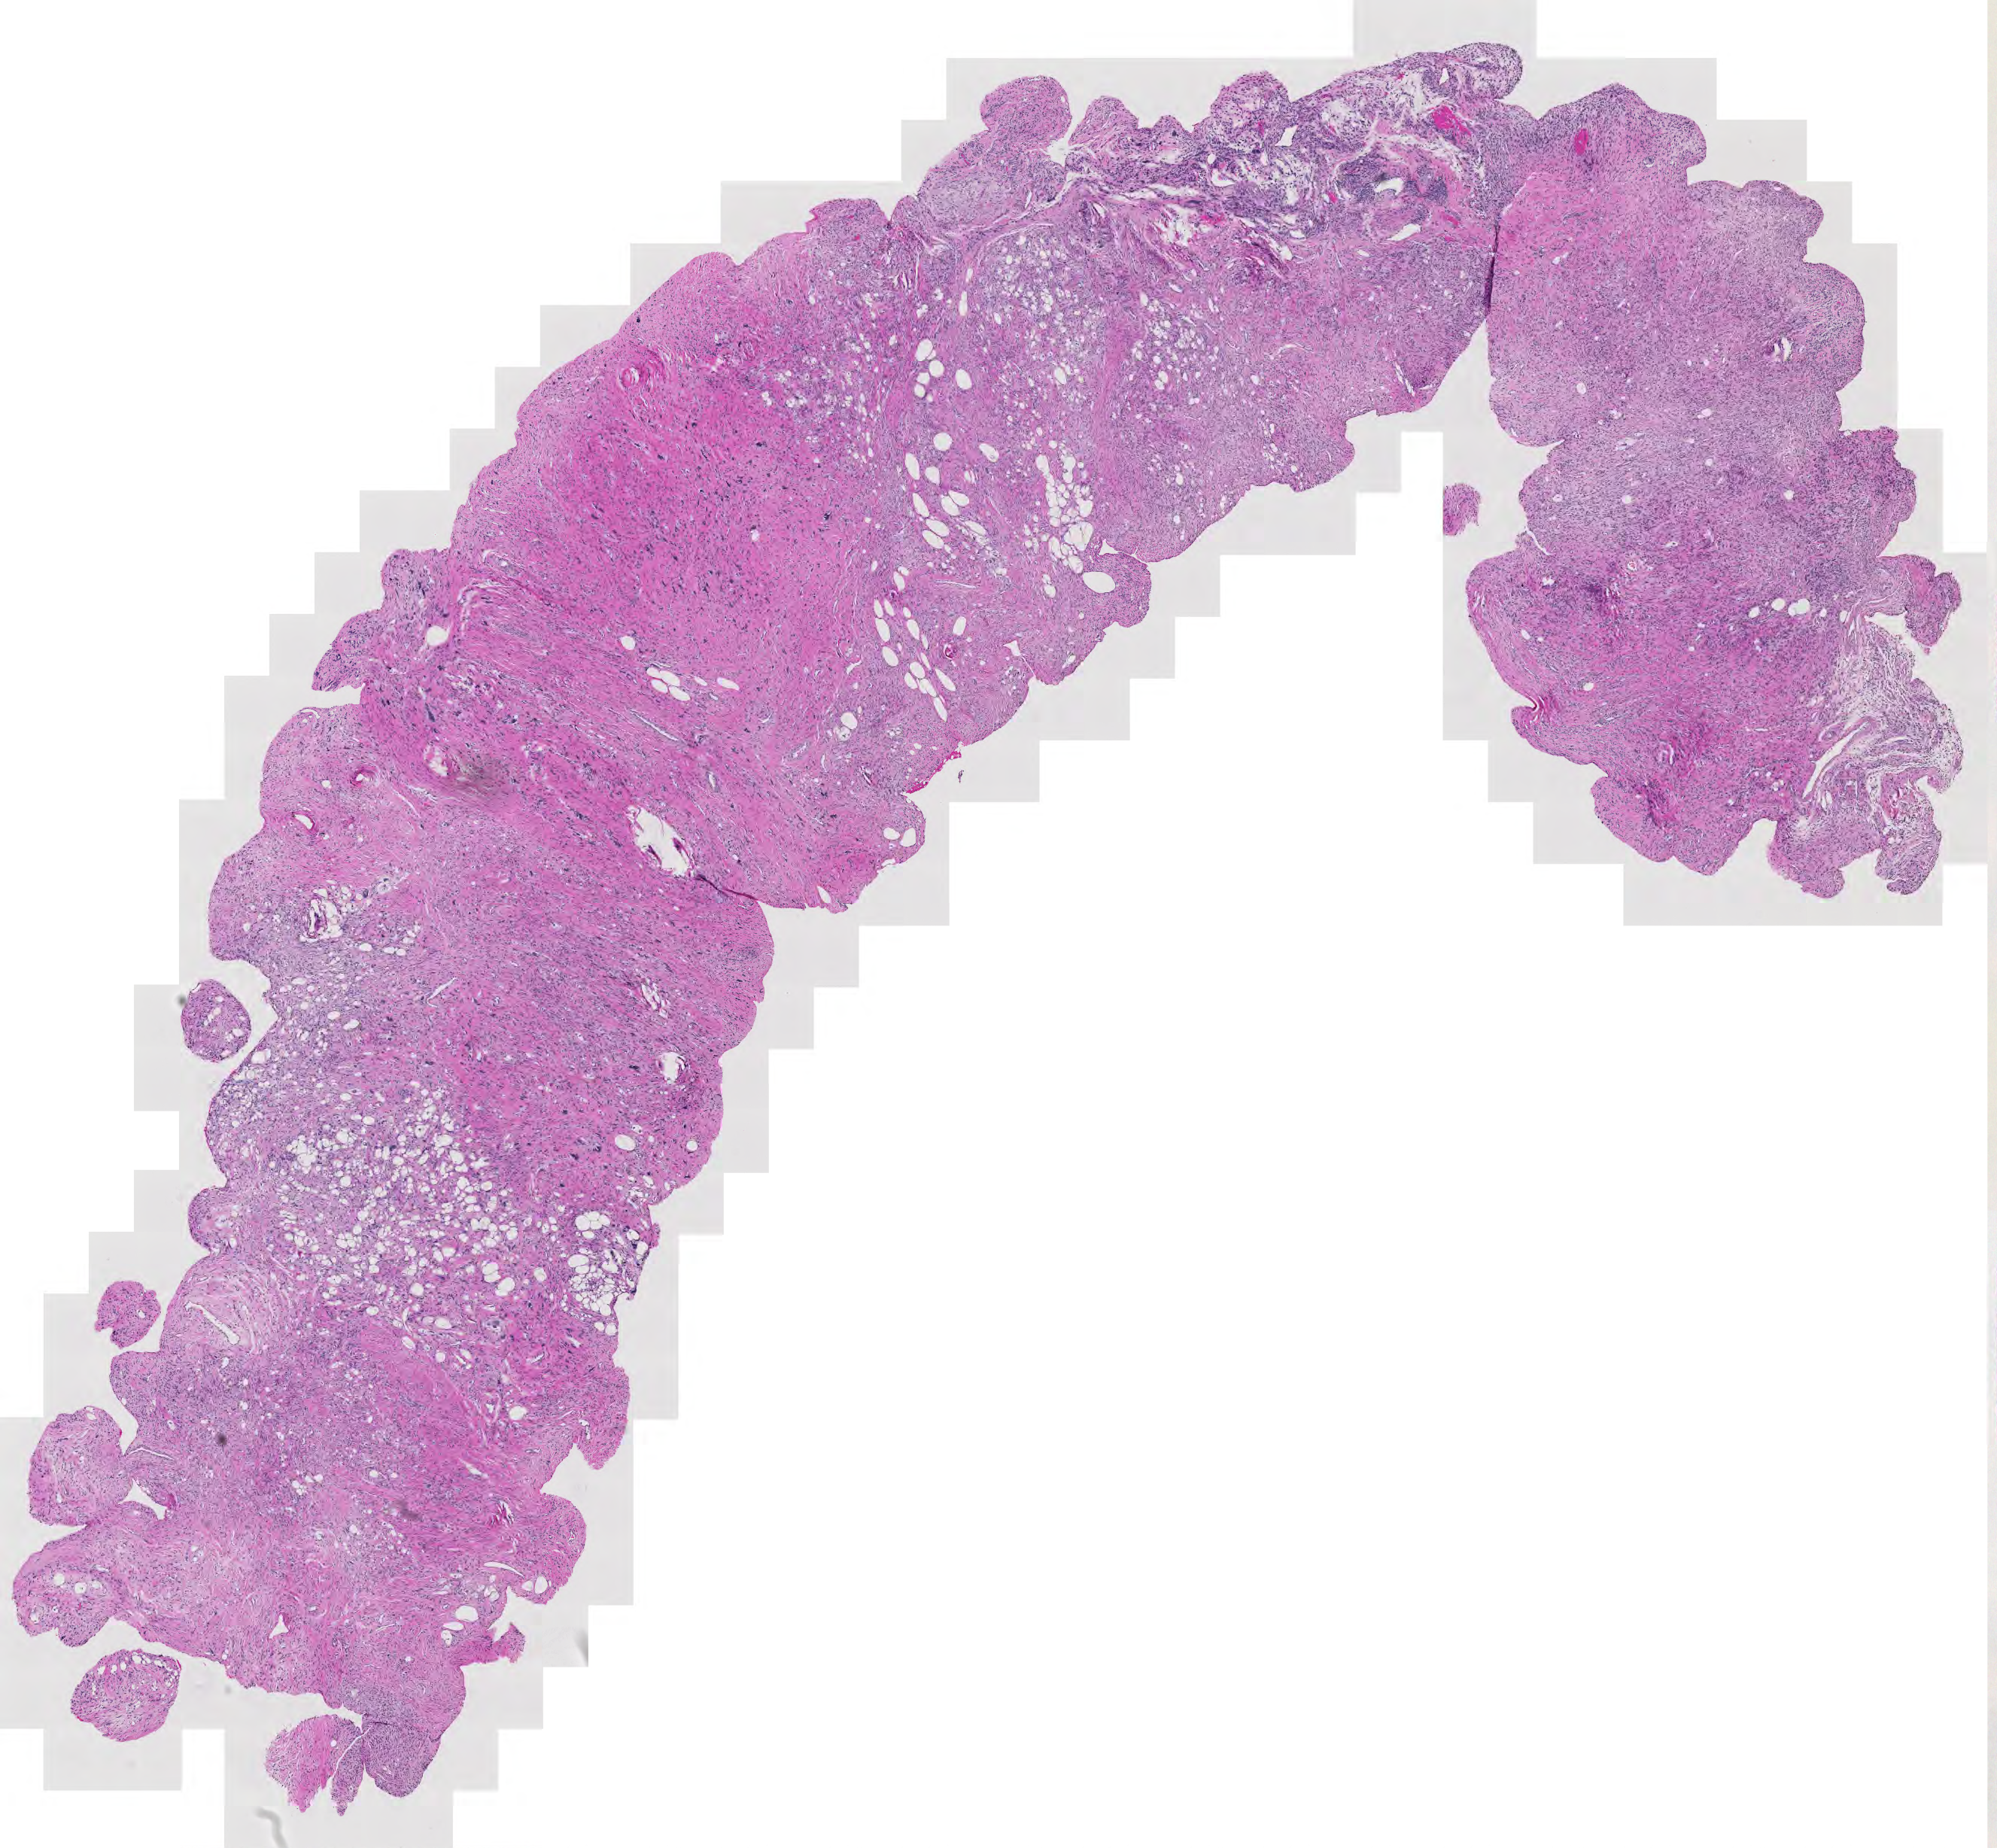
Digitized Hematoxylin and eosin (H&E) stained tissue section (whole slide) — shown as a low-resolution overview of the whole scanned area (about 13.7 x 12.7 mm, slide scanned at 20x). Tumour tissue sample. Male, 74 y/o.
Patient diagnosis (cohort enrolment): sarcoma (site not recorded at cohort level). Primary tumour site (as recorded): upper extremity.